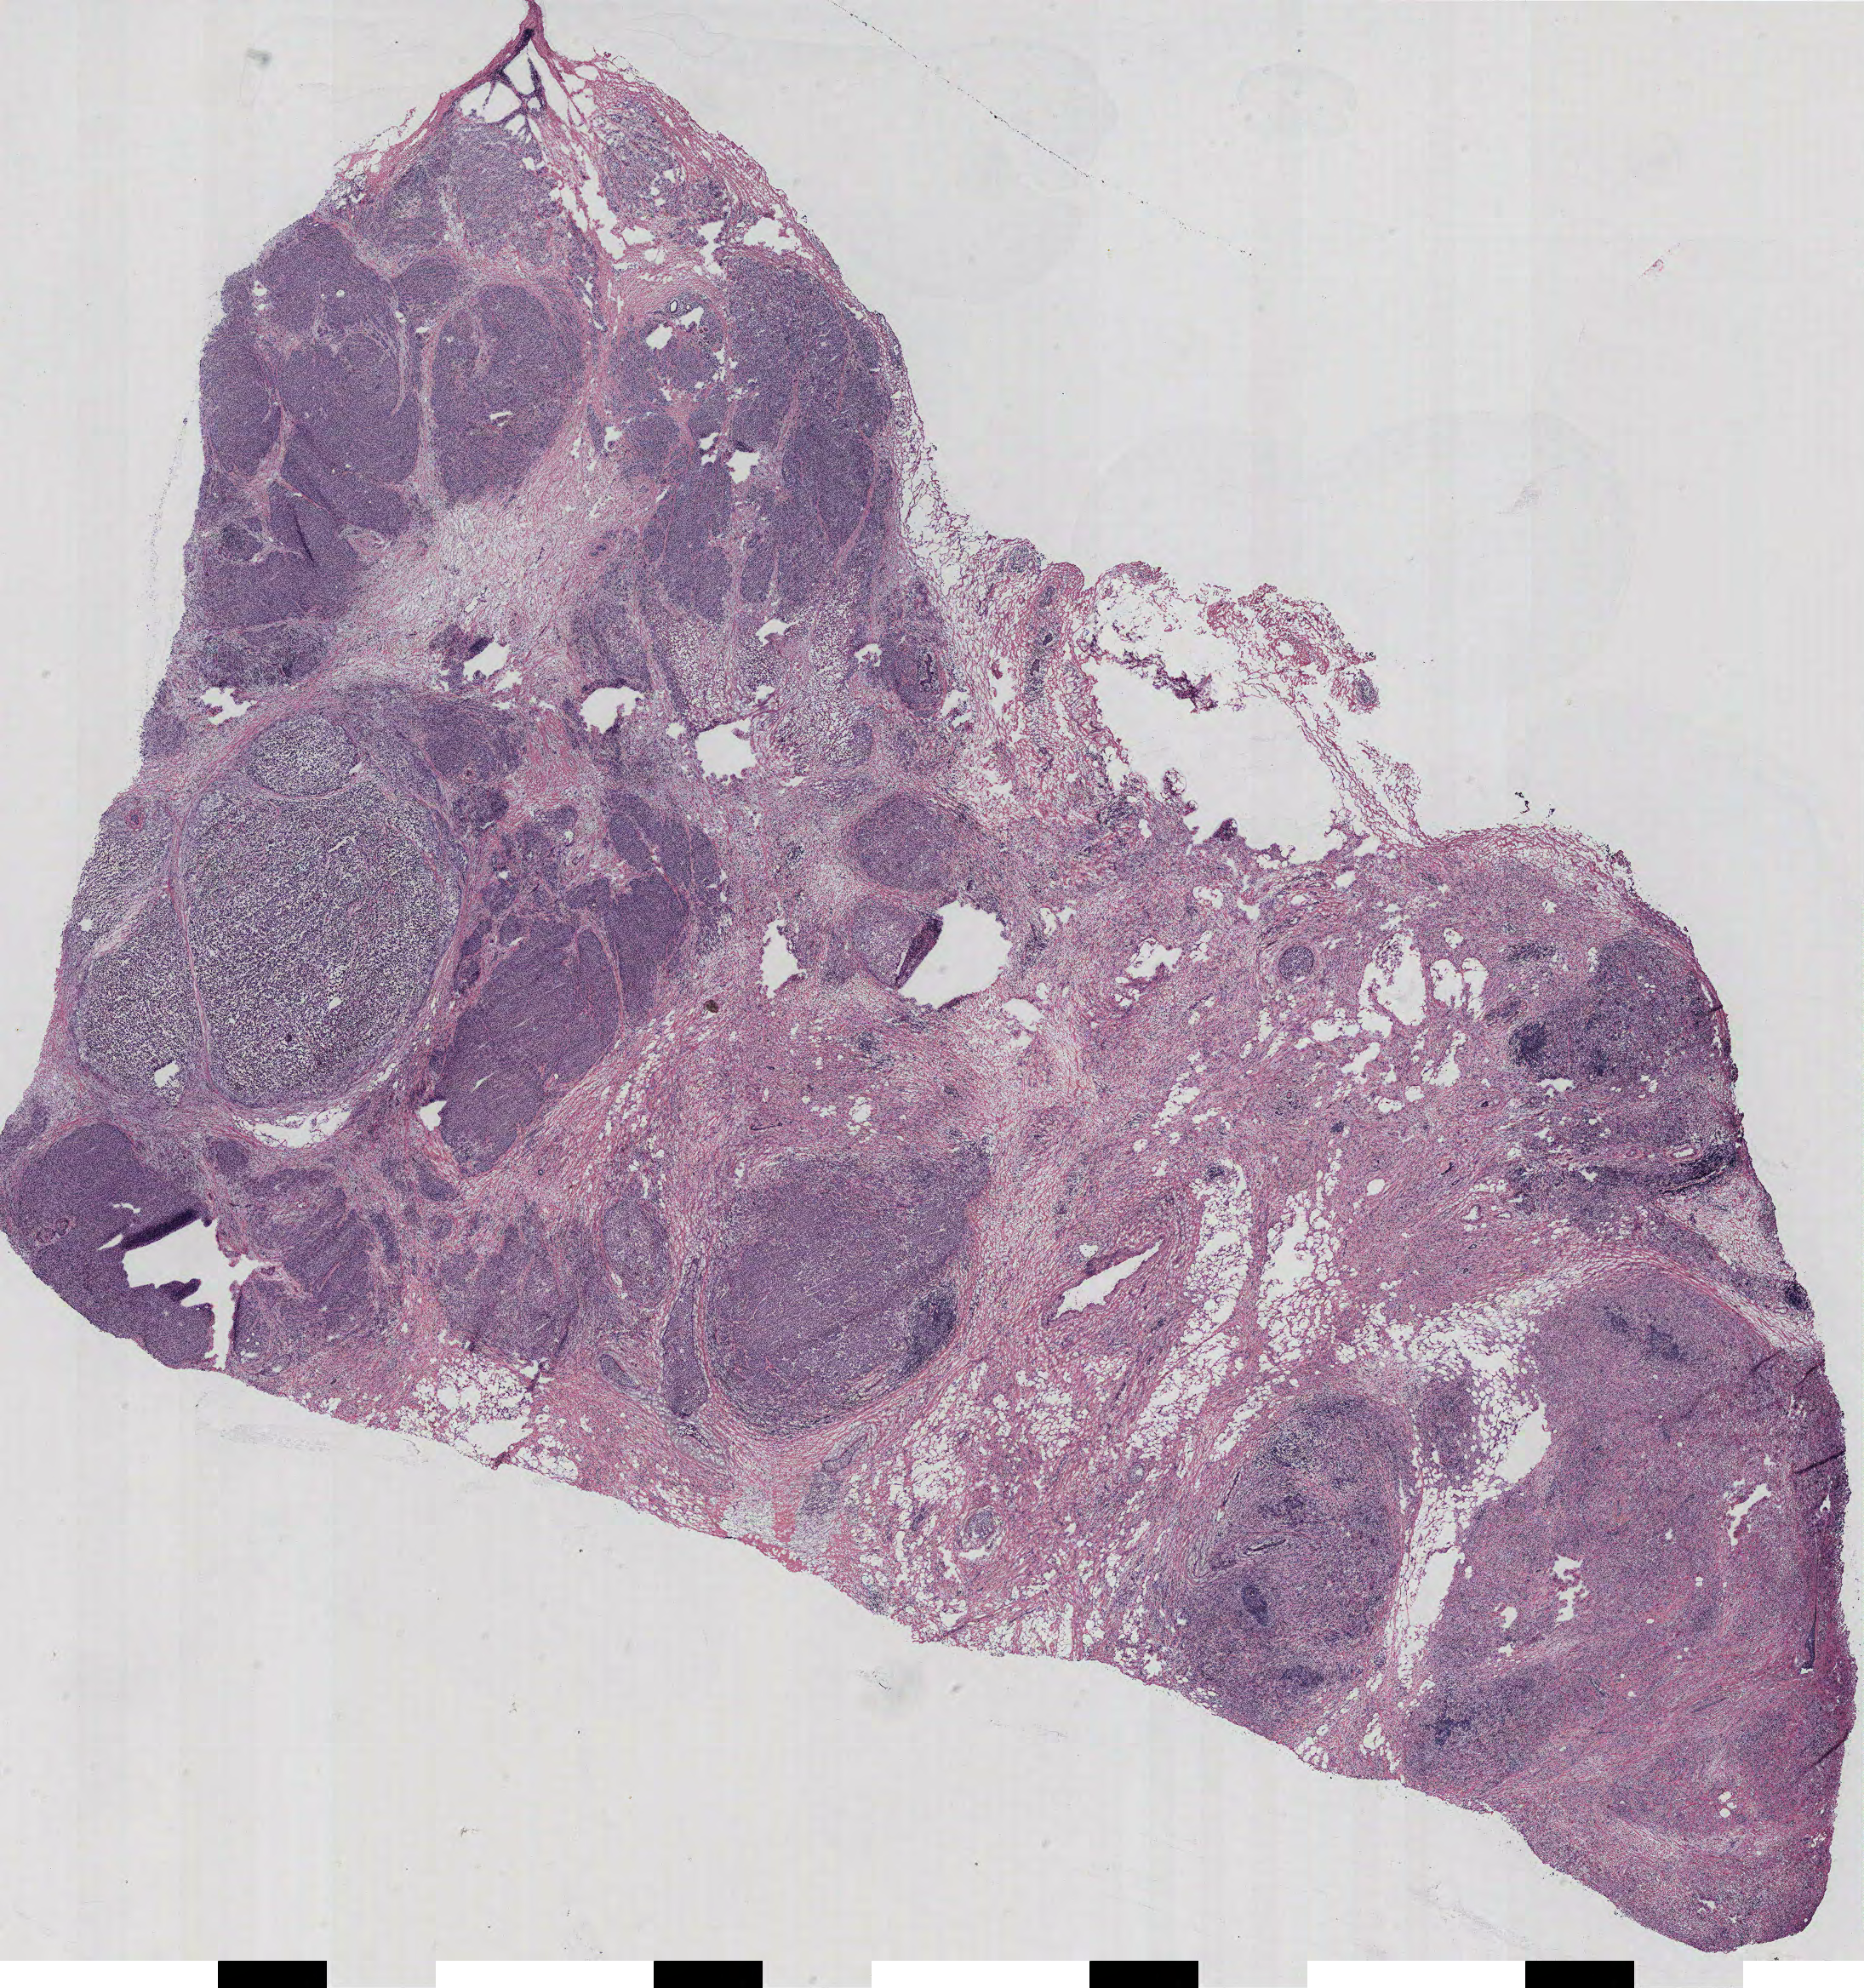
H&E-stained whole-slide image — low-resolution overview of the scanned area, about 17.5 x 18.7 mm. Breast, tissue type not recorded. Patient: female, age 65 years.
• patient diagnosis: Infiltrating duct carcinoma, NOS